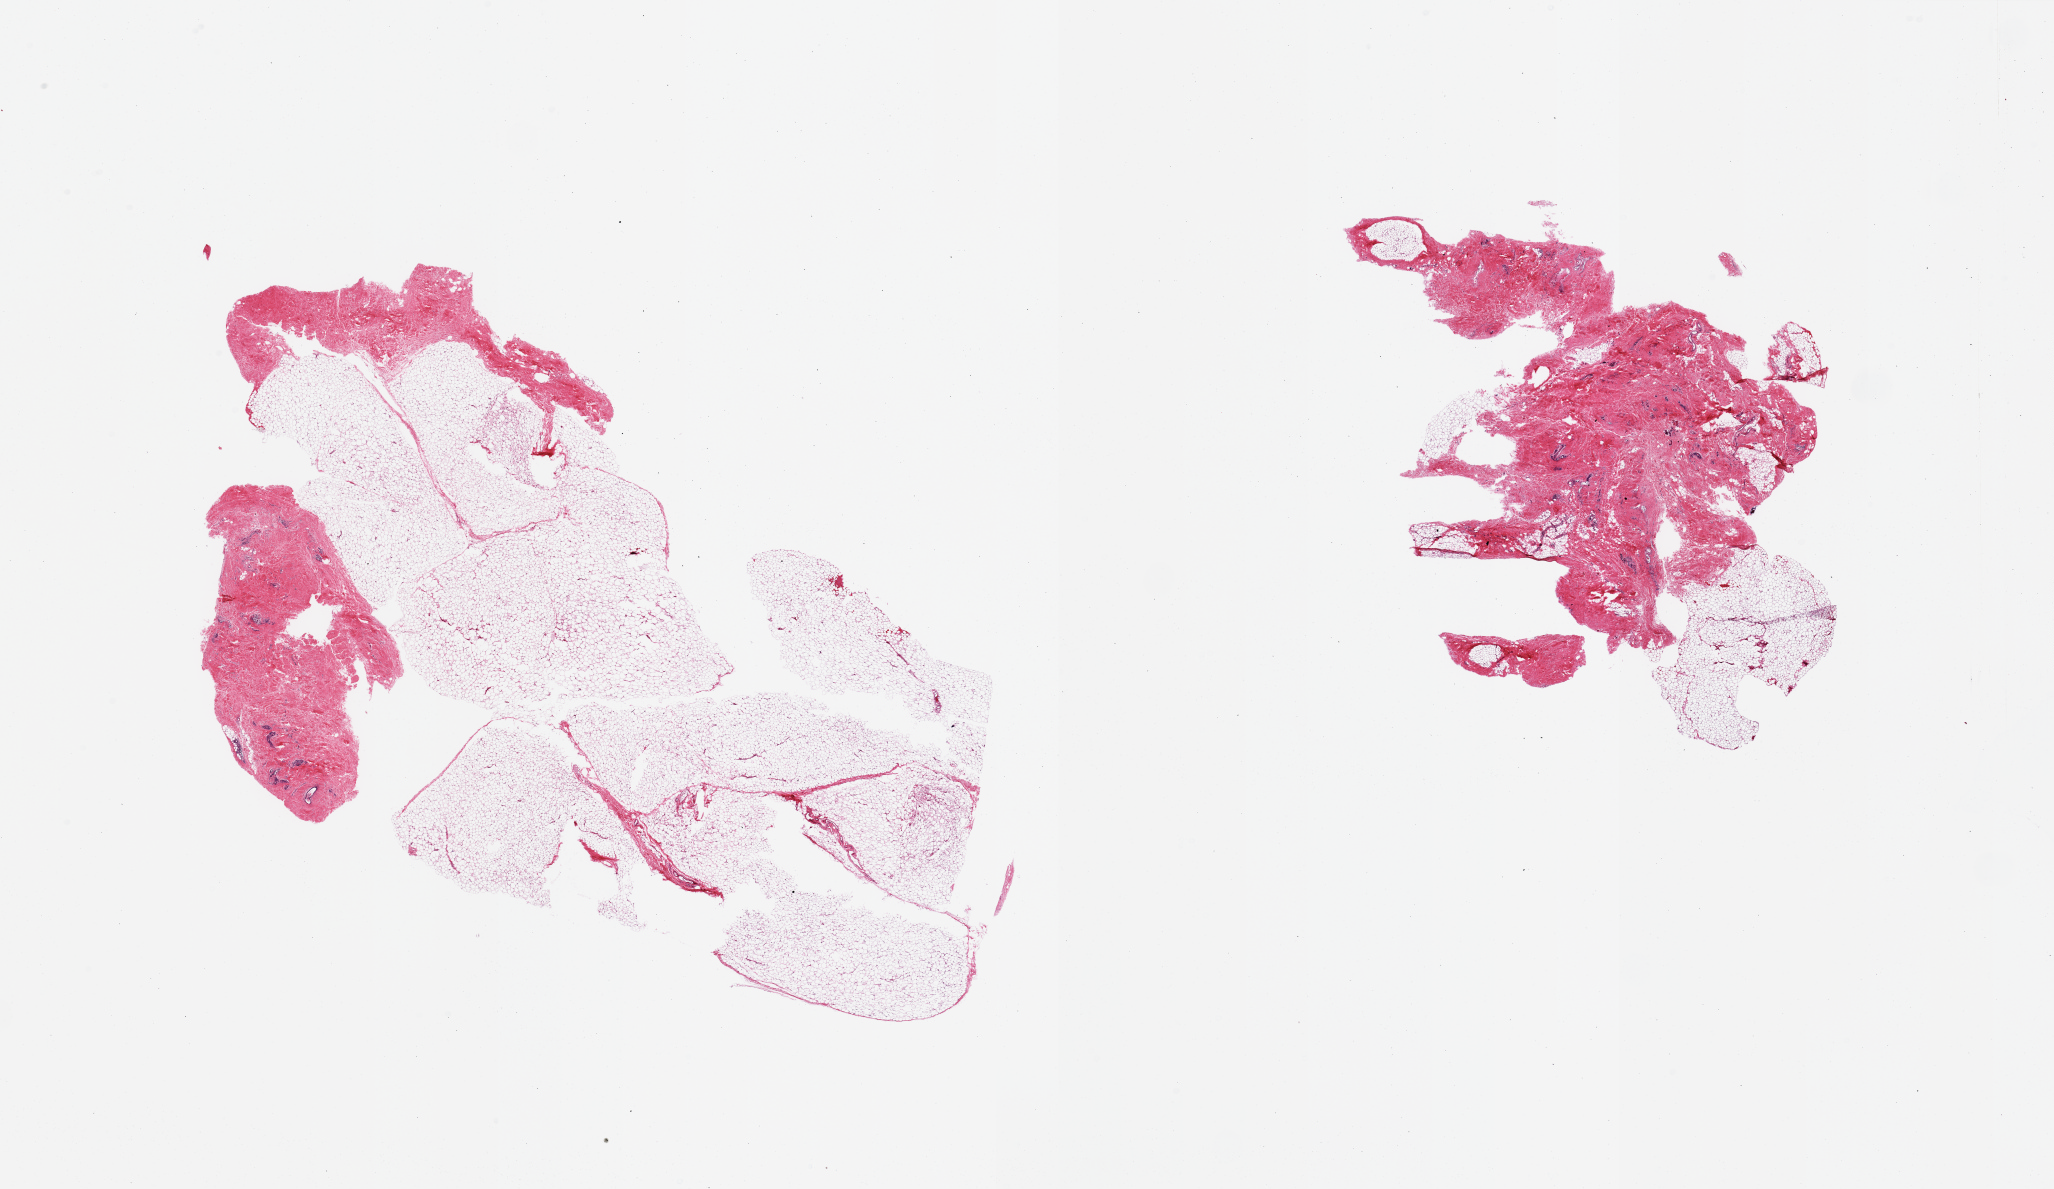
Digitized H&E-stained section — a low-resolution overview of the entire scanned area, about 32.5 x 18.8 mm (slide scanned at 20x). PAXgene-fixed paraffin-embedded (PFPE) section. Section of breast (target tissue). Donor tissue sample. Donor sex: female.
Review note (as recorded): 2 pieces, fibrous mastopathy.